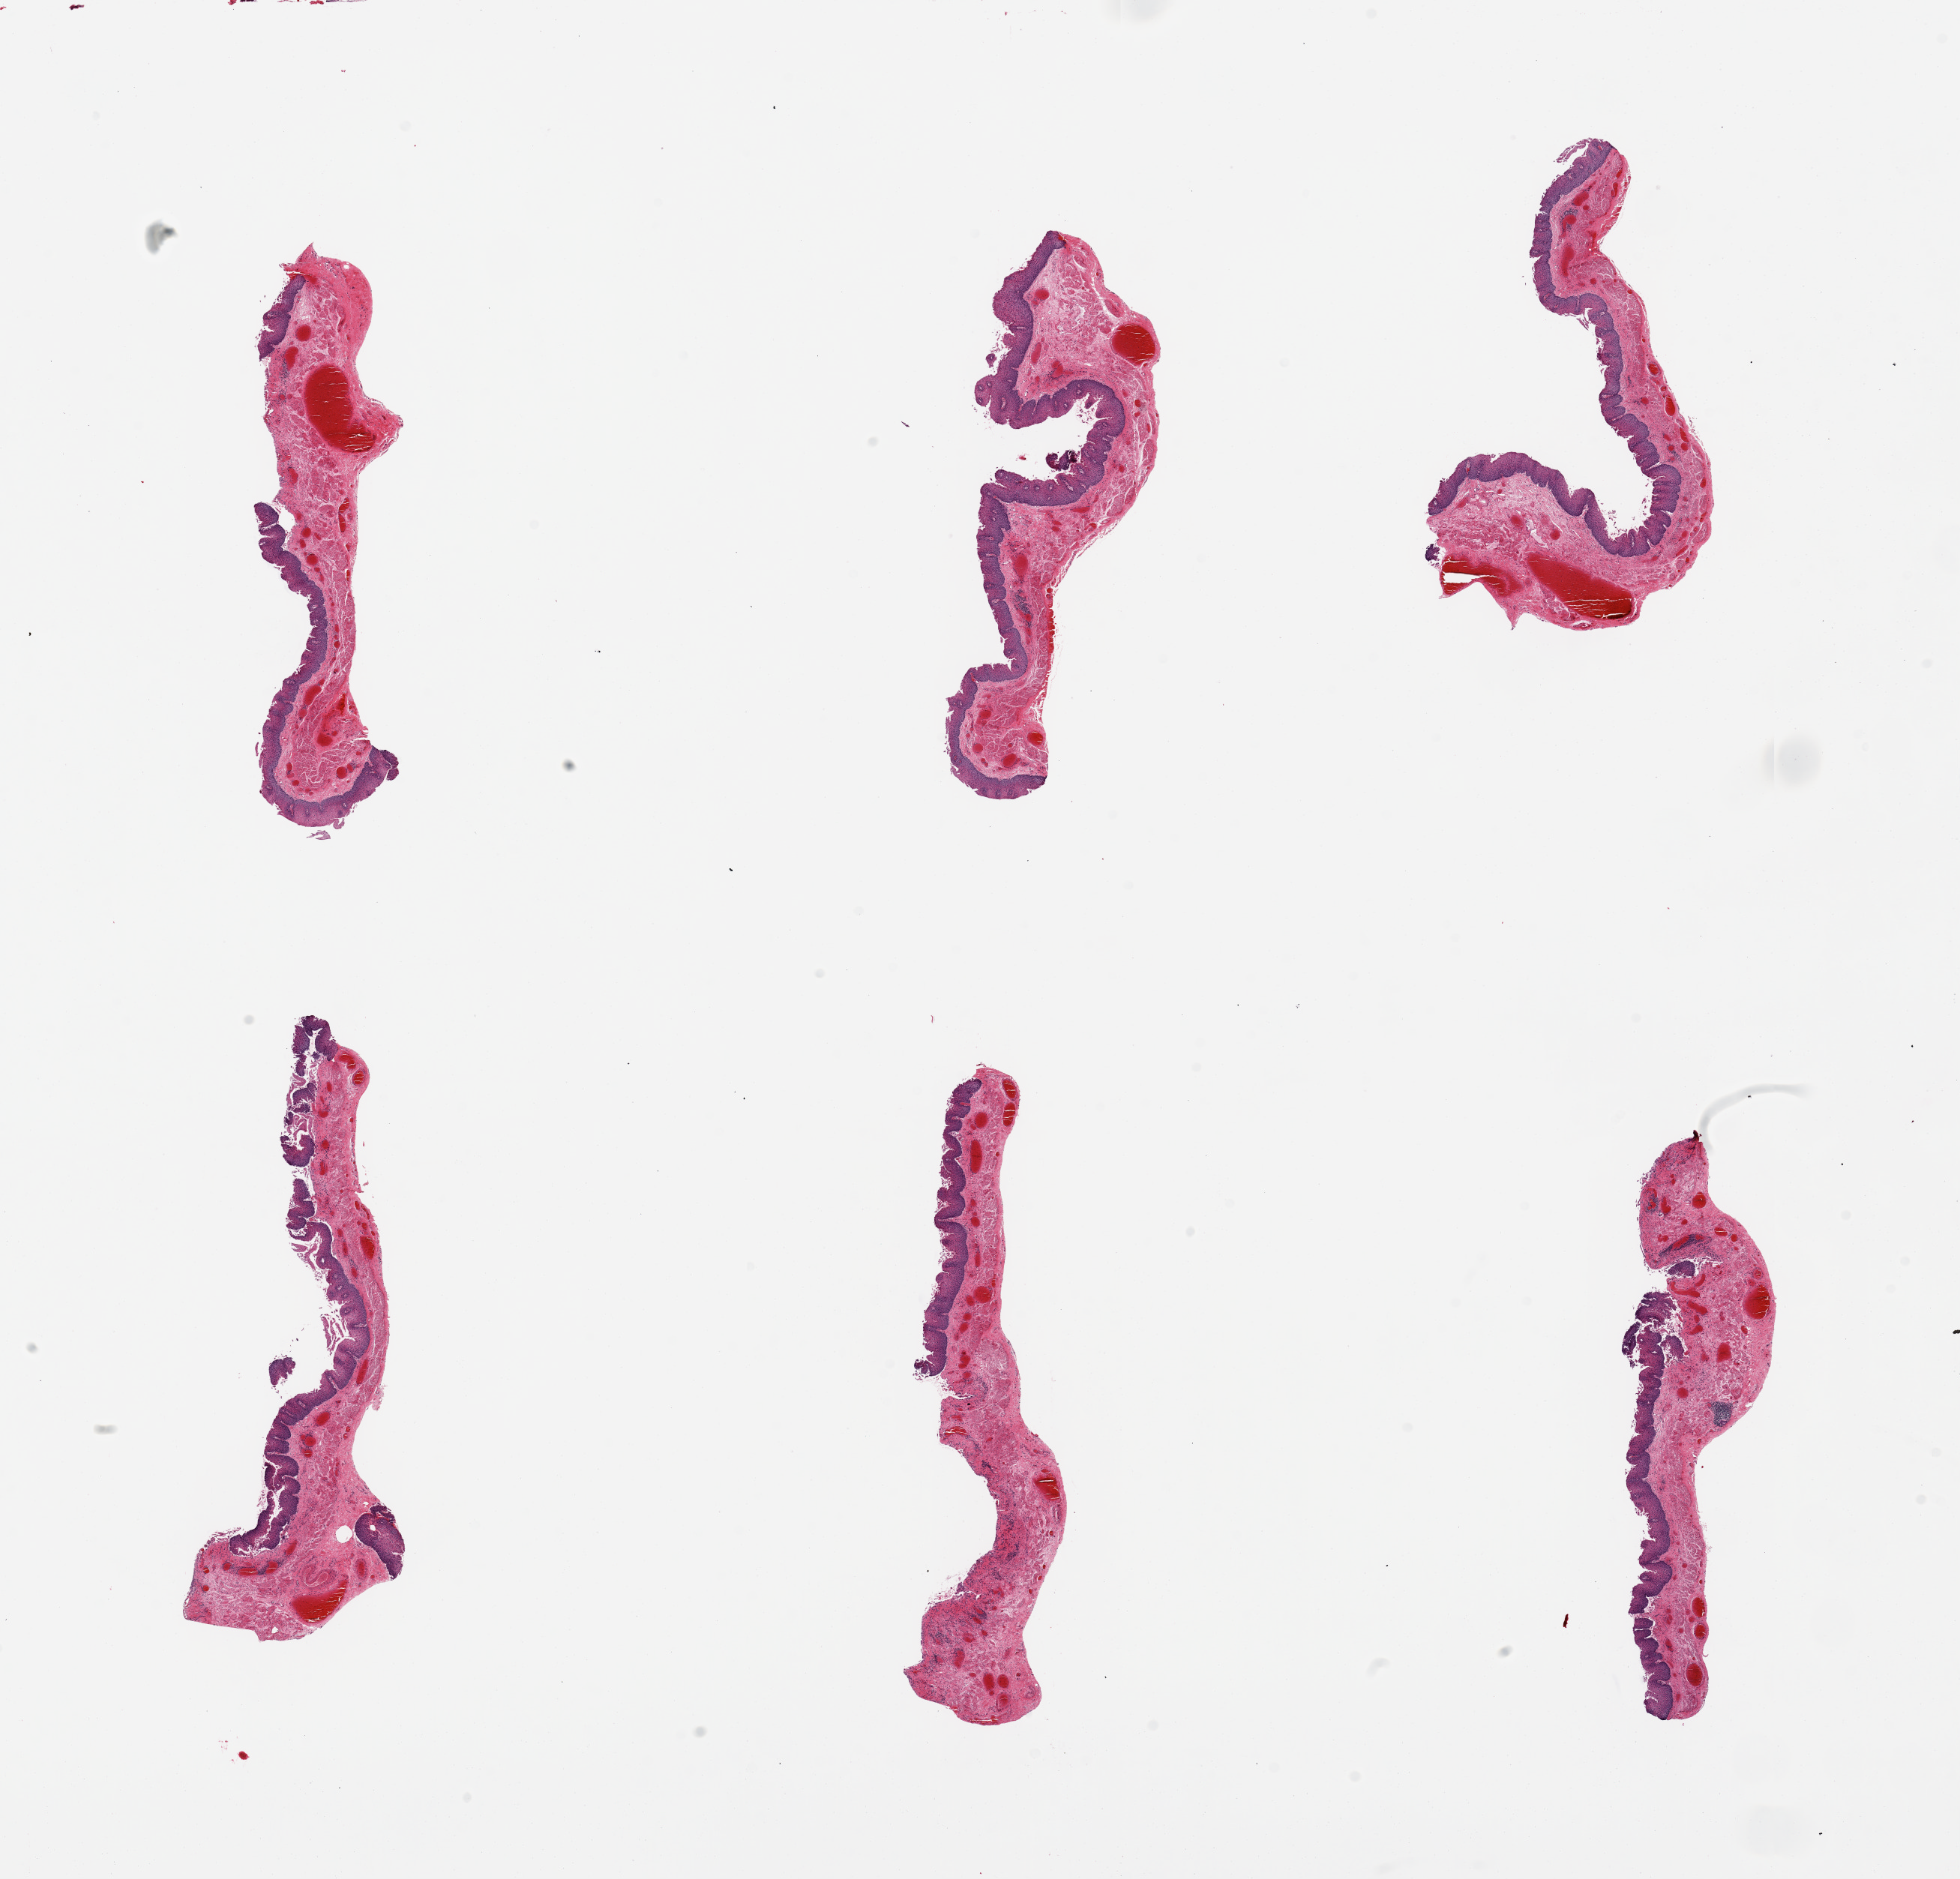
Whole-slide image, haematoxylin and eosin stain — a low-resolution overview of the entire scanned area, about 20.7 x 19.8 mm; PAXgene-fixed, paraffin-embedded tissue; section of esophageal mucous membrane (target tissue); donor tissue sample. Male donor.
- pathologist's review note for this sample: 6 pieces, up to 7x2mm; squamous mucosa ~20 % ot thickness